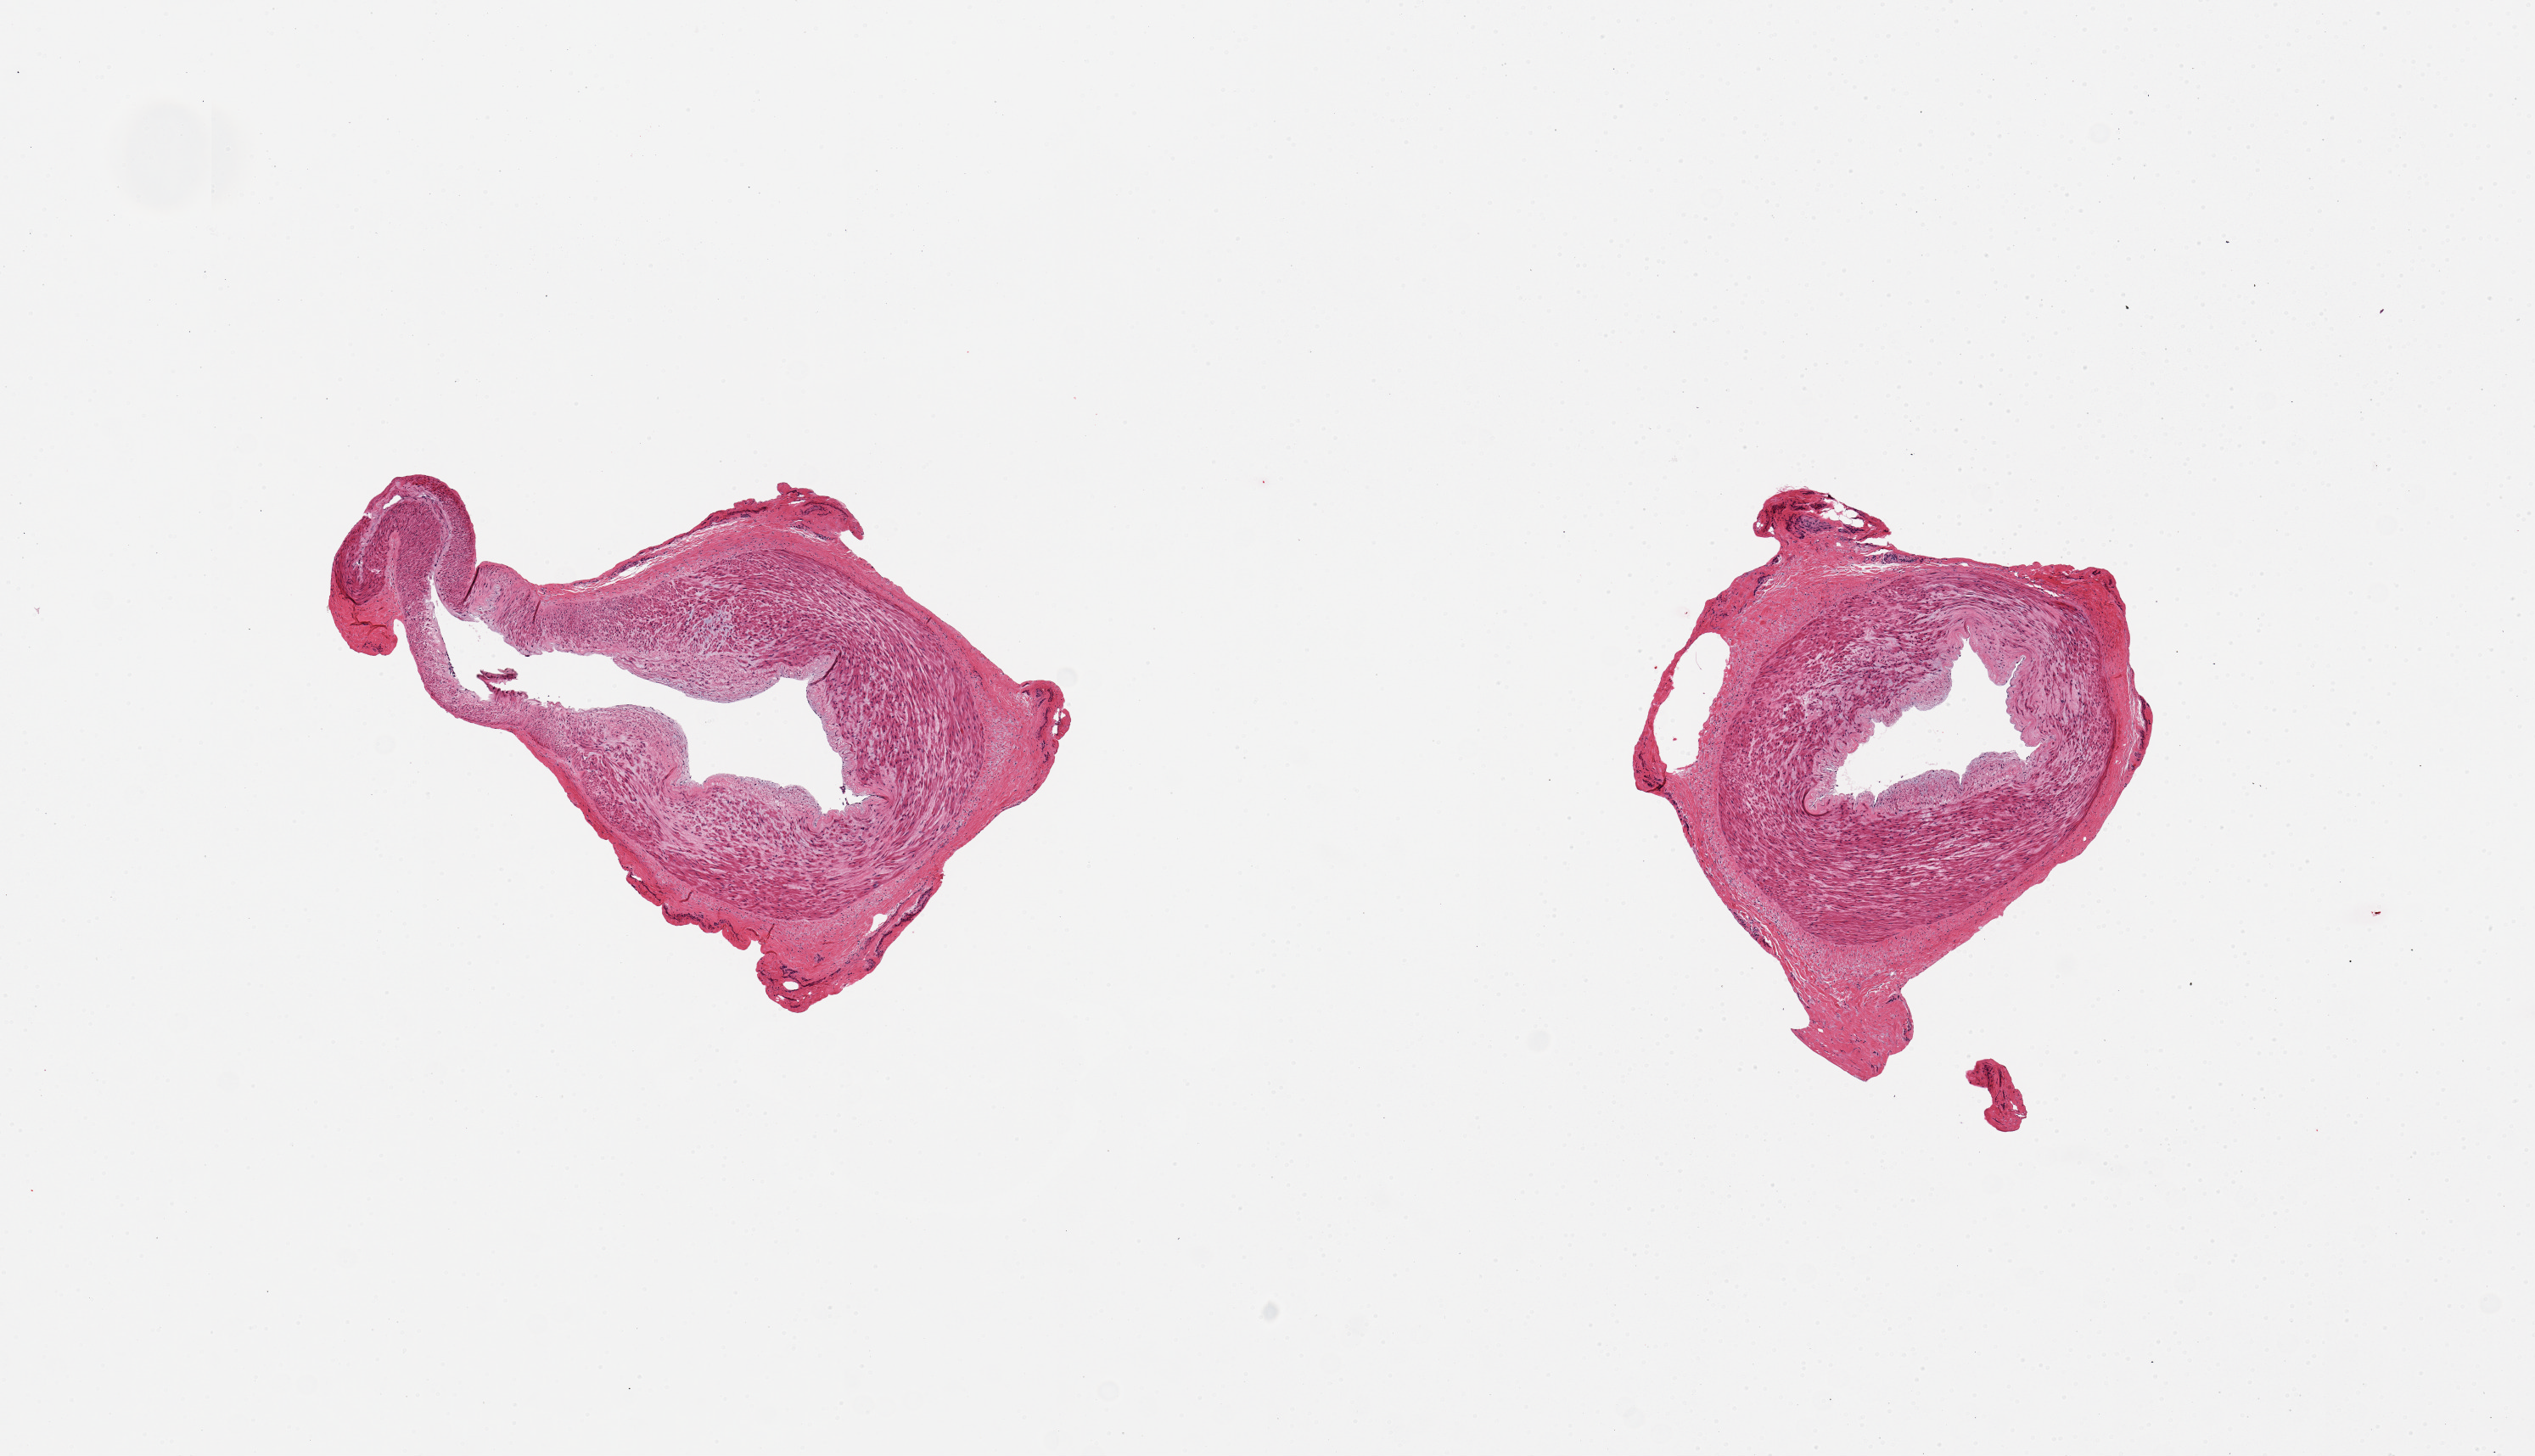
Whole-slide image, hematoxylin and eosin (H&E) stain, brightfield, a low-resolution overview of the entire scanned area, about 11.8 x 6.8 mm, PAXgene-fixed, paraffin-embedded tissue, section of tibial artery (target tissue), tissue donor sample. Donor sex: male.
Review note (as recorded): 2 pieces, 3.5x2 and 2x2mm, ~1.5mm d. Minimal adherent fibrous tissue /fat.